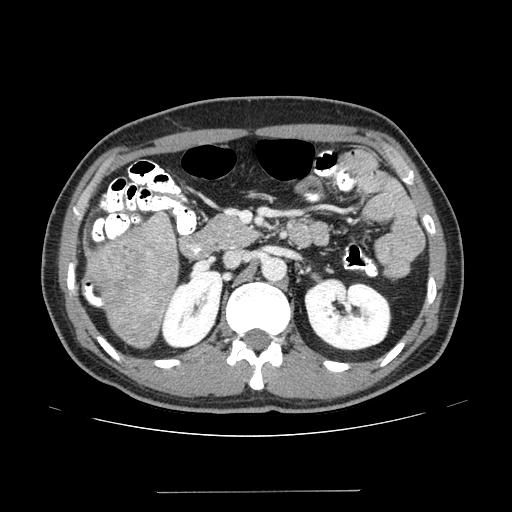
Contrast-enhanced abdominal CT (liver protocol), one axial slice; slice 64 of 131 in the series (ordered by position); reconstruction kernel STANDARD; one of 2 acquisitions stored at this slice position; soft-tissue window (W 400 / L 40 HU); 512 × 512 image matrix, field of view 380 × 380 mm. From the clinical record (not read from this slice): diagnosis: hepatocellular carcinoma (patient treated with transarterial chemoembolisation; whether this scan precedes or follows treatment is not stated here); TNM stage (as recorded): Stage-I; Child-Pugh class: A; tumour nodularity: uninodular.
Outlined on this slice (semi-automatically segmented with operator editing):
- liver parenchyma outside the tumour (the mass and vessels are separate outlines, so this box may not span the whole liver): bounding box <84,214,178,348> (left, top, right, bottom; pixels)
- mass: <89,233,156,284>